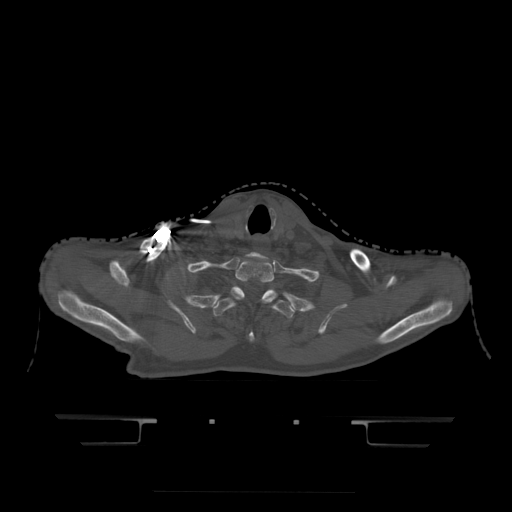
CT including the spine, one axial slice; position 394 of 522 along the scan axis; bone window (W 1800 / L 400 HU); 512 × 512 image matrix, field of view 436 × 436 mm. Patient age 68 years. Case-level facts recorded for this patient, not image findings: primary cancer: urothelial.
Outlined on this slice (semi-automatic segmentation, software-assisted and operator-edited):
- T1 vertebra: bounding box [x1, y1, x2, y2] px = [231, 259, 278, 298]
- T2 vertebra: [214, 287, 295, 343]